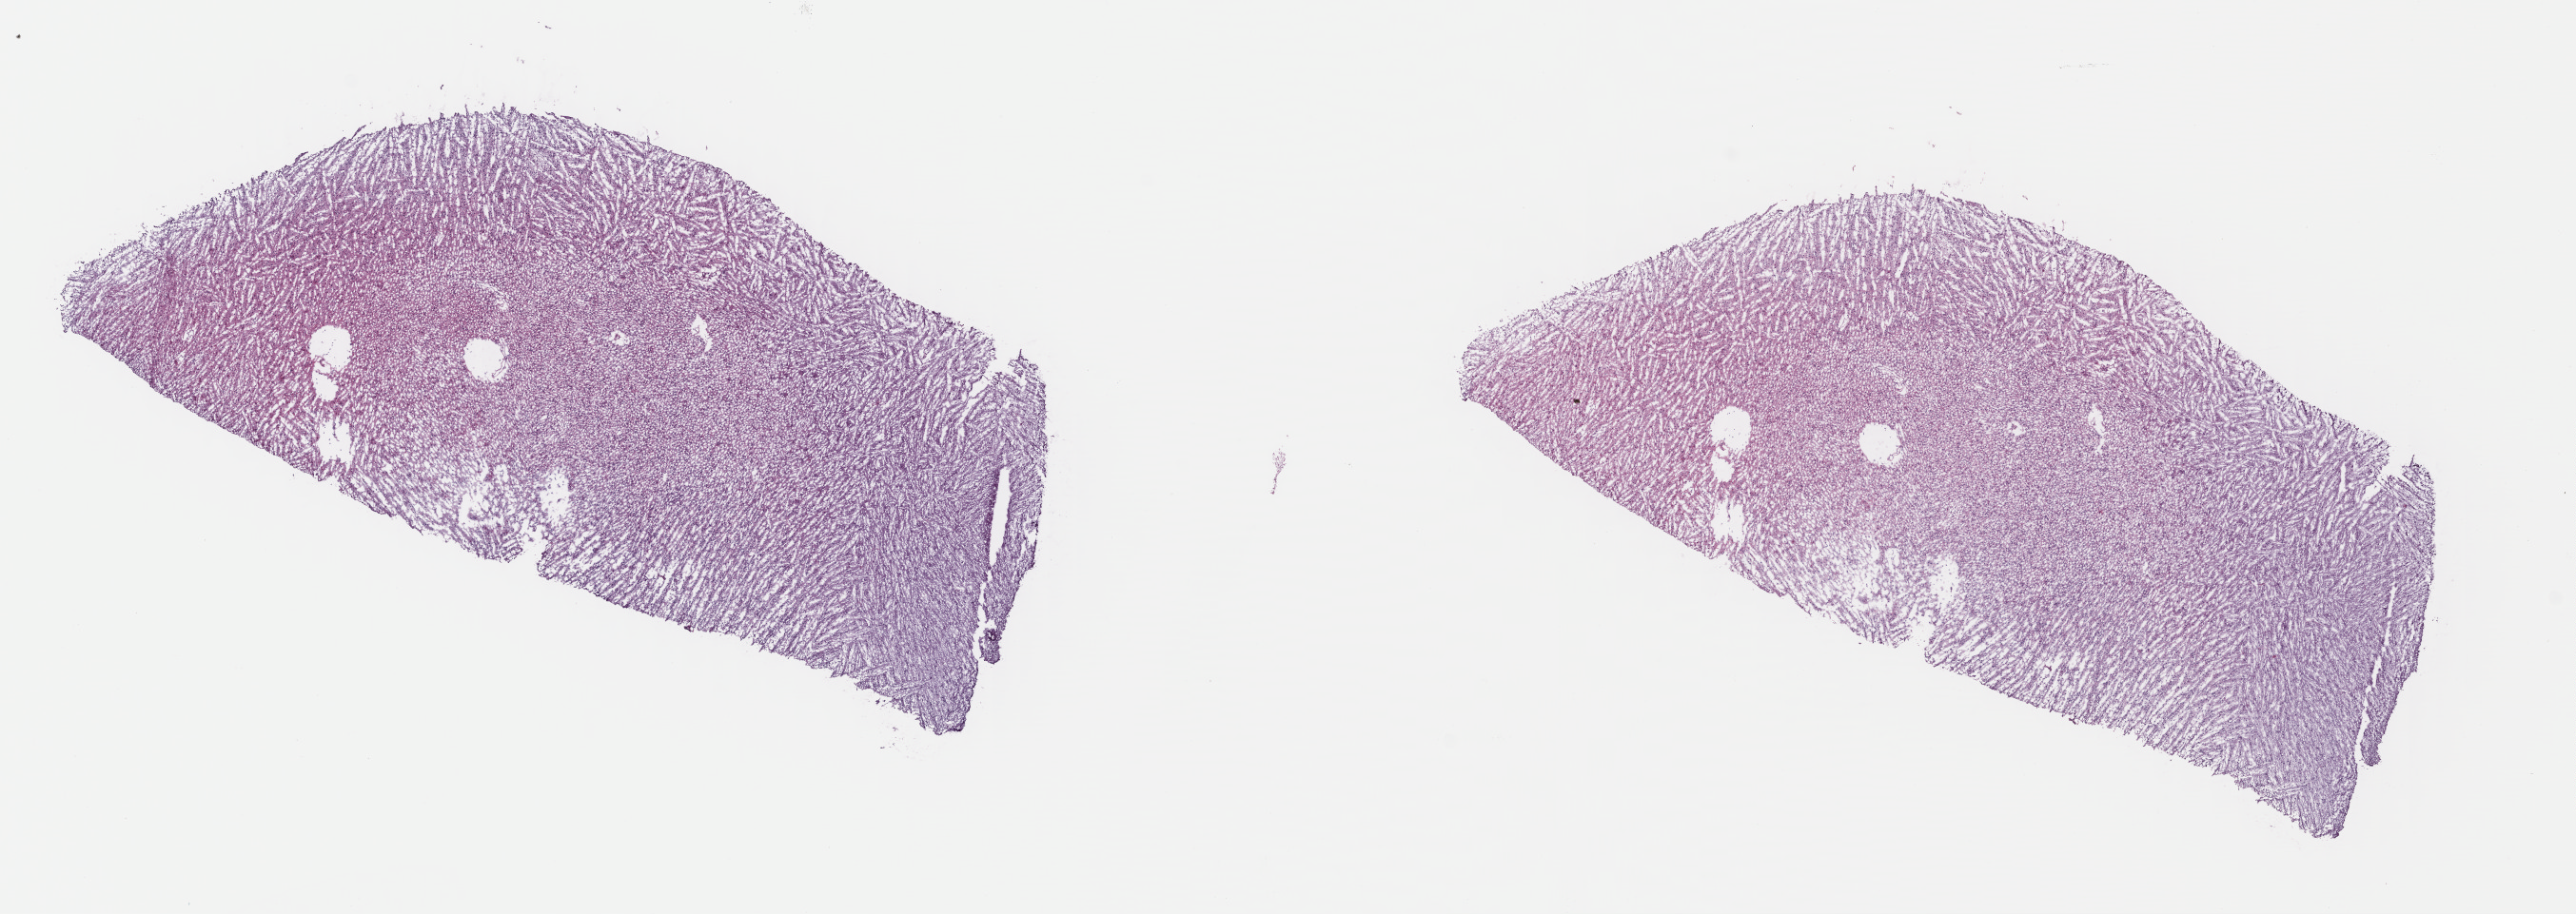
H&E whole-slide image, a low-resolution overview of the entire scanned area, about 21.3 x 7.6 mm. Frozen section from the top of the tissue portion. Primary tumour sample from the brain. Patient: female, age at initial diagnosis 31 years. Histologic grade: G2 (moderately differentiated). Slide review estimates, as recorded: tumour cells 70%, tumour nuclei 80%, normal cells 5%, stromal cells 25%, necrosis 0%. Inflammatory infiltration, as recorded: lymphocyte infiltration 0%, monocyte infiltration 0%, neutrophil infiltration 0%.
Pathologic diagnosis: Mixed glioma.